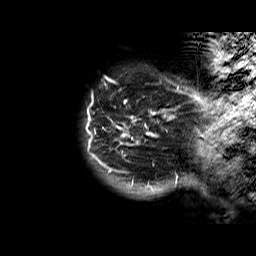
Breast MRI (dynamic contrast-enhanced), one sagittal slice; position 1 of 60 along the scan axis; dynamic contrast-enhanced series, time point 2 of 6 at this slice position (early post-contrast); 1.5 T; TE 6.3 ms, TR 32.4 ms; 4 mm slice thickness; 256 × 256 image matrix, field of view 200 × 200 mm. Female patient. Case-level facts recorded for this patient, not image findings: setting: breast cancer imaged before/during neoadjuvant chemotherapy; receptor status: HR-positive, HER2-negative.
Structures marked on this image (semi-automatic segmentation, software-assisted and operator-edited):
- analysis volume of interest (the breast-tissue region the enhancement analysis was run in; not a lesion): bounding box <87,76,177,183> (left, top, right, bottom; pixels)
- tumour enhancement mask (voxels above the 100 % enhancement threshold inside the analysis volume of interest): <87,77,177,183>